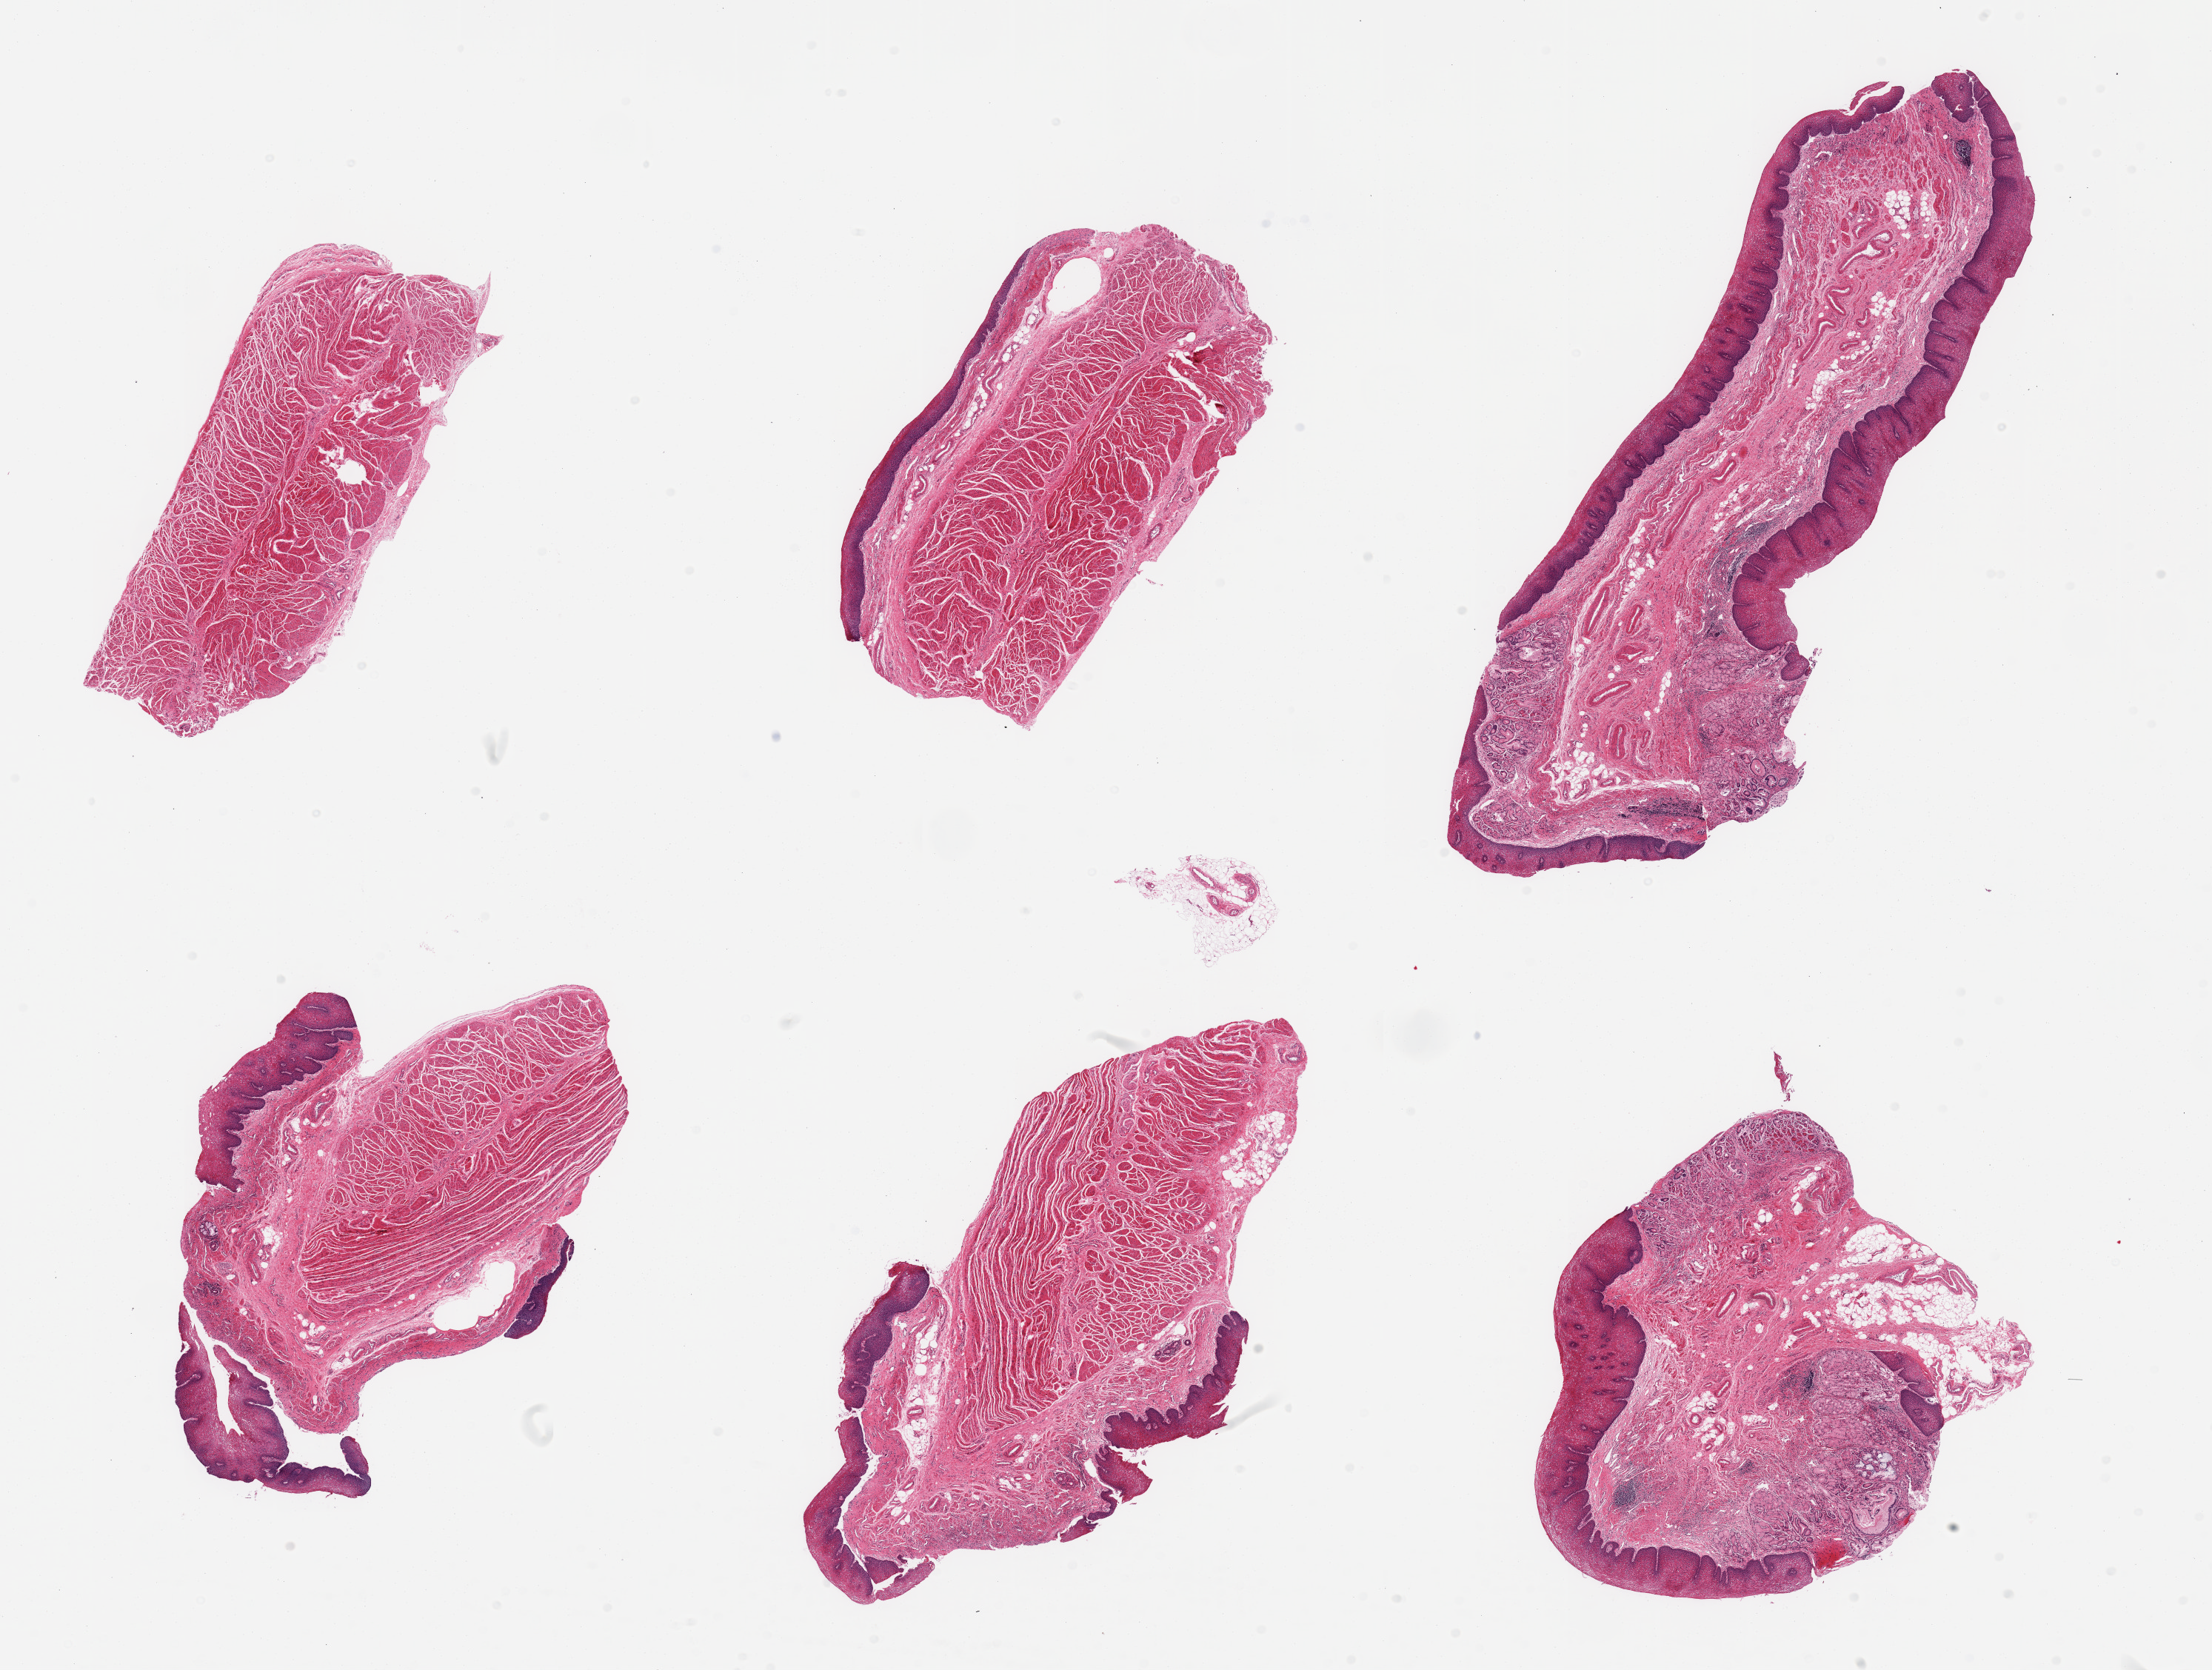
Digitized haematoxylin and eosin-stained section, brightfield, whole scanned area (about 23.6 x 17.8 mm, acquisition: 20x scan) shown as a low-resolution overview, PAXgene-fixed, paraffin-embedded tissue, section of gastroesophageal junction (target tissue), tissue donor sample. Donor: male.
* pathologist's review note for this sample: 5 pieces, confirmed target muscularis; ~10% contaminant mucosa